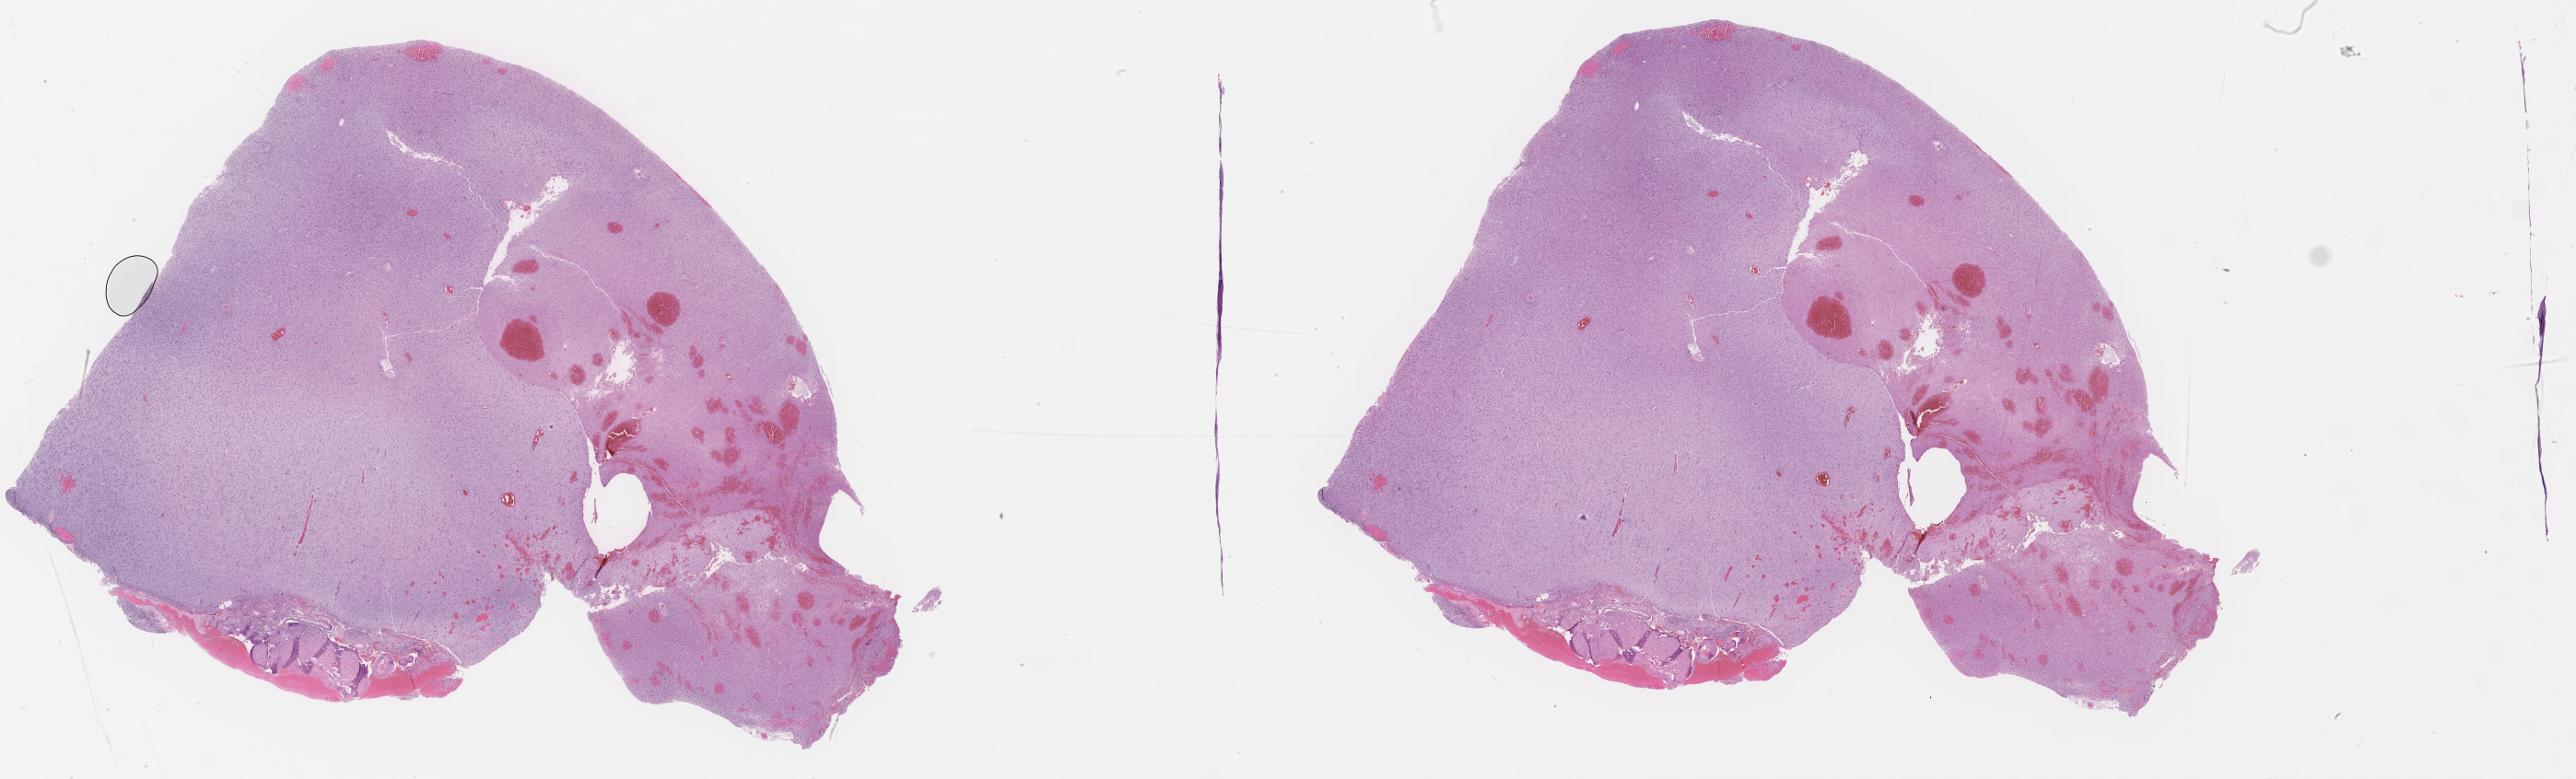
Whole-slide histology image, H&E-stained, low-resolution overview of the scanned area, about 45.0 x 13.6 mm; formalin-fixed paraffin-embedded (FFPE) diagnostic section; brain, primary tumour sample. Female patient; age at initial diagnosis 53 years. Histologic grade: G2 (moderately differentiated).
• diagnosis: Oligodendroglioma, NOS (cerebrum)